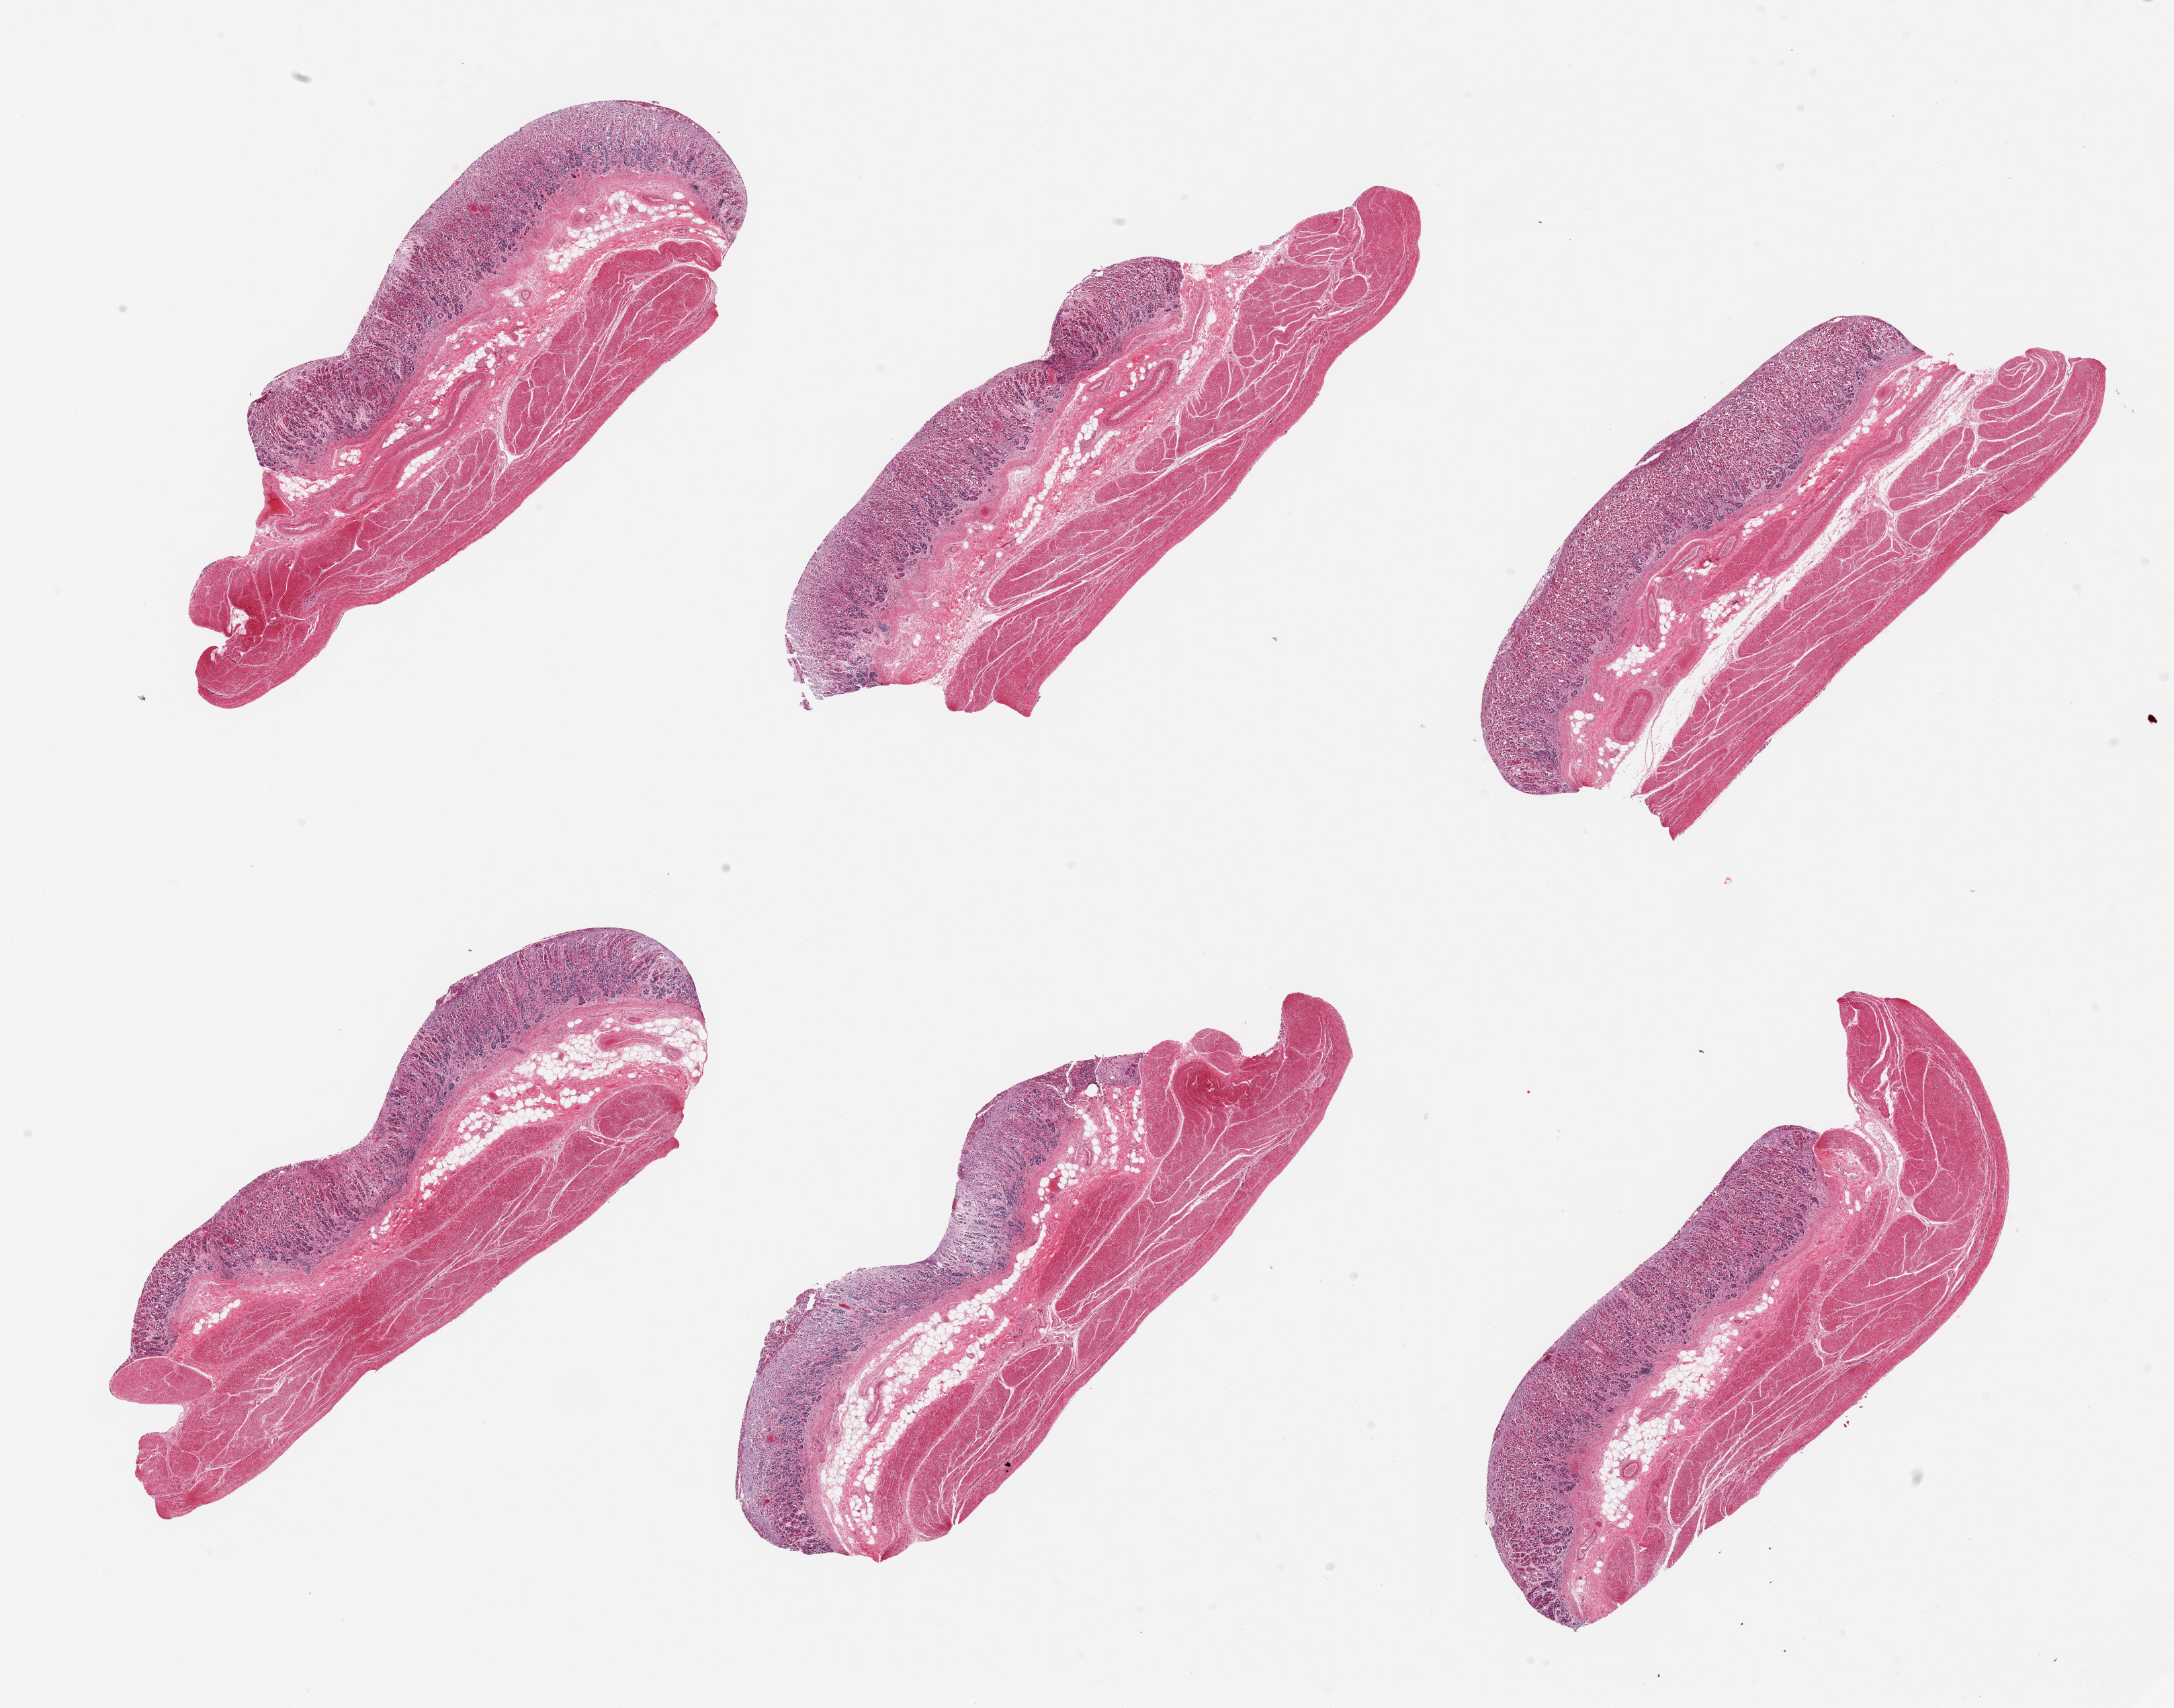
H&E whole-slide image, low-resolution overview of the scanned area, about 25.6 x 20.1 mm (acquisition: 20x scan), PAXgene-fixed paraffin-embedded (PFPE) section, target tissue: stomach, tissue donor sample. Female donor.
Pathologist's review note for this sample: 6 pieces; mucosa autolyzed, muscle intact but partially autolyzed (2).